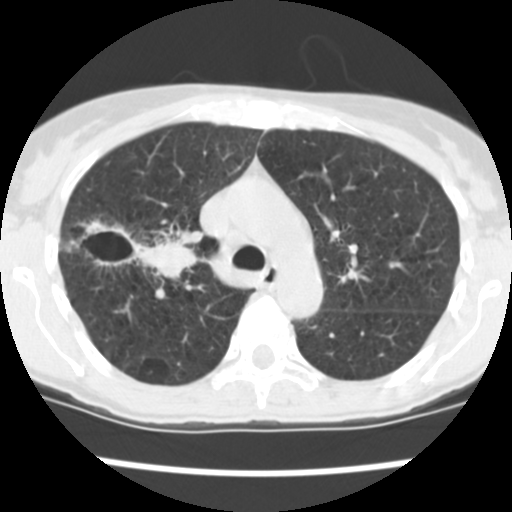
Axial slice from a low-dose chest CT screening exam. First (baseline) screen. Lung window (W 1500 / L -600 HU). 2.5 mm slice thickness. Standard (soft-tissue) reconstruction kernel (STANDARD). 512 × 512 image matrix, field of view 276 × 276 mm. Female participant, aged 60 years at enrolment.
Expert reader's lesion annotation, bounding box [x1, y1, x2, y2] px = [83, 216, 195, 284]. The screening reader recorded 3 non-calcified nodules or masses ≥4 mm on this exam (right upper lobe, right upper lobe, right lower lobe); which of them this box marks is not recorded. Official screen result: positive, change unspecified: nodule(s) >= 4 mm or enlarging nodule(s), mass(es), or other non-specific abnormalities suspicious for lung cancer. Participant outcome: lung cancer diagnosed 19 days after this screen — non-small cell carcinoma, right upper lobe, stage IV (AJCC 6th edition), 26 mm at pathology.